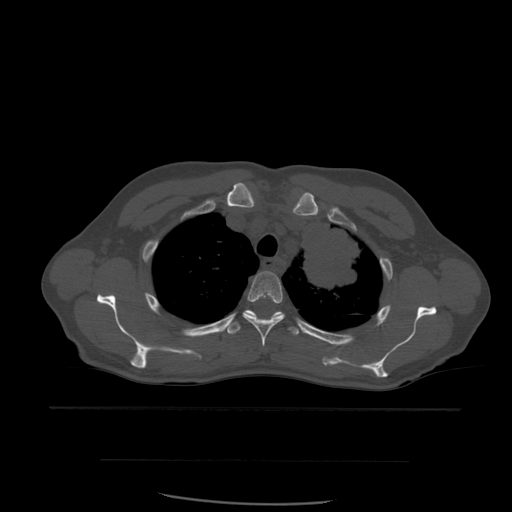
CT including the spine, one axial slice; position 439 of 574 along the scan axis; bone window (W 1800 / L 400 HU); 1.25 mm slice thickness; 512 × 512 image matrix, field of view 392 × 392 mm. Patient age 48 years. From the clinical record (not read from this slice): primary cancer: lung.
Structures marked on this image (semi-automatically segmented with operator editing):
- T3 vertebra: bounding box (x1, y1, x2, y2) in pixels: (243, 272, 284, 347)
- T4 vertebra: (224, 310, 300, 336)